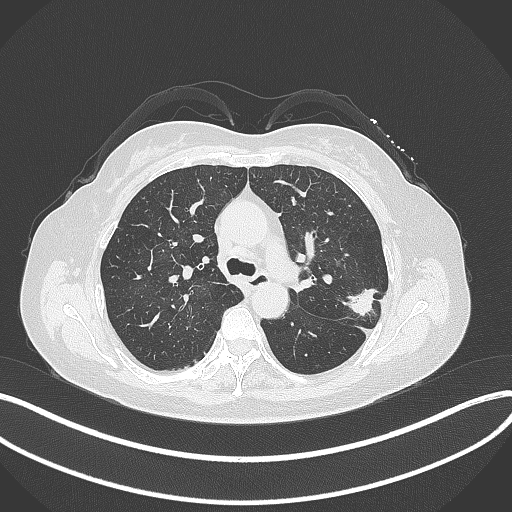
Chest CT, one axial slice. Position 215 of 319 along the scan axis. Reconstruction kernel B70f. 120 kVp. Lung window (W 1500 / L -600 HU). 1 mm slice thickness. 512 × 512 image matrix, field of view 400 × 400 mm. Patient: female, 60 years. From the clinical record (not read from this slice): clinical TNM (as recorded): T1c N0 M0.
Structures marked on this image (bounding box drawn by a radiologist):
- lung tumour (recorded histology: adenocarcinoma): bounding box [x1, y1, x2, y2] px = [343, 283, 380, 319]